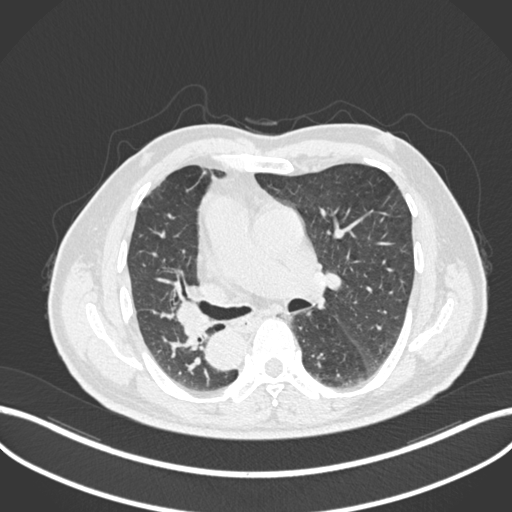
Chest CT, one axial slice; position 126 of 206 along the scan axis; reconstruction kernel B30f; 120 kVp; lung window (W 1500 / L -600 HU); 1 mm slice thickness; 512 × 512 image matrix. Male patient, age 67 years. Case-level facts recorded for this patient, not image findings: clinical TNM (as recorded): T2a N0 M0.
Outlined on this slice (rectangle marked by the reading radiologist):
- lung tumour (recorded histology: squamous cell carcinoma): bounding box [x1, y1, x2, y2] px = [169, 296, 208, 350]